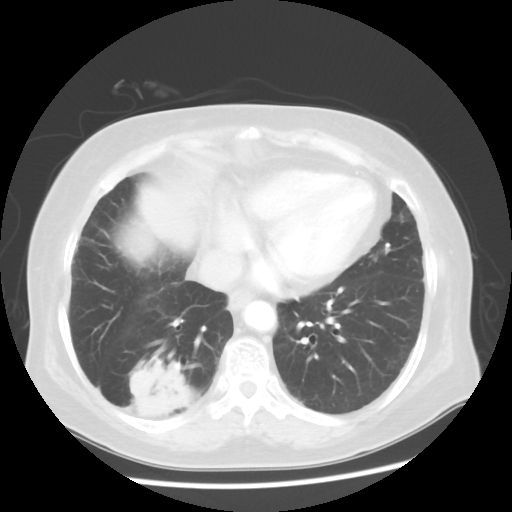
Chest CT, one axial slice. Position 19 of 56 along the scan axis. Reconstruction kernel STANDARD. Lung window (W 1500 / L -600 HU). 5 mm slice thickness. 512 × 512 image matrix, field of view 360 × 360 mm. Female patient, age 64 years. From the clinical record (not read from this slice): clinical TNM (as recorded): Tis N0 M0.
Annotated regions visible in this slice (rectangle marked by the reading radiologist):
- lung tumour (recorded histology: adenocarcinoma): bounding box (x1, y1, x2, y2) in pixels: (125, 352, 201, 430)